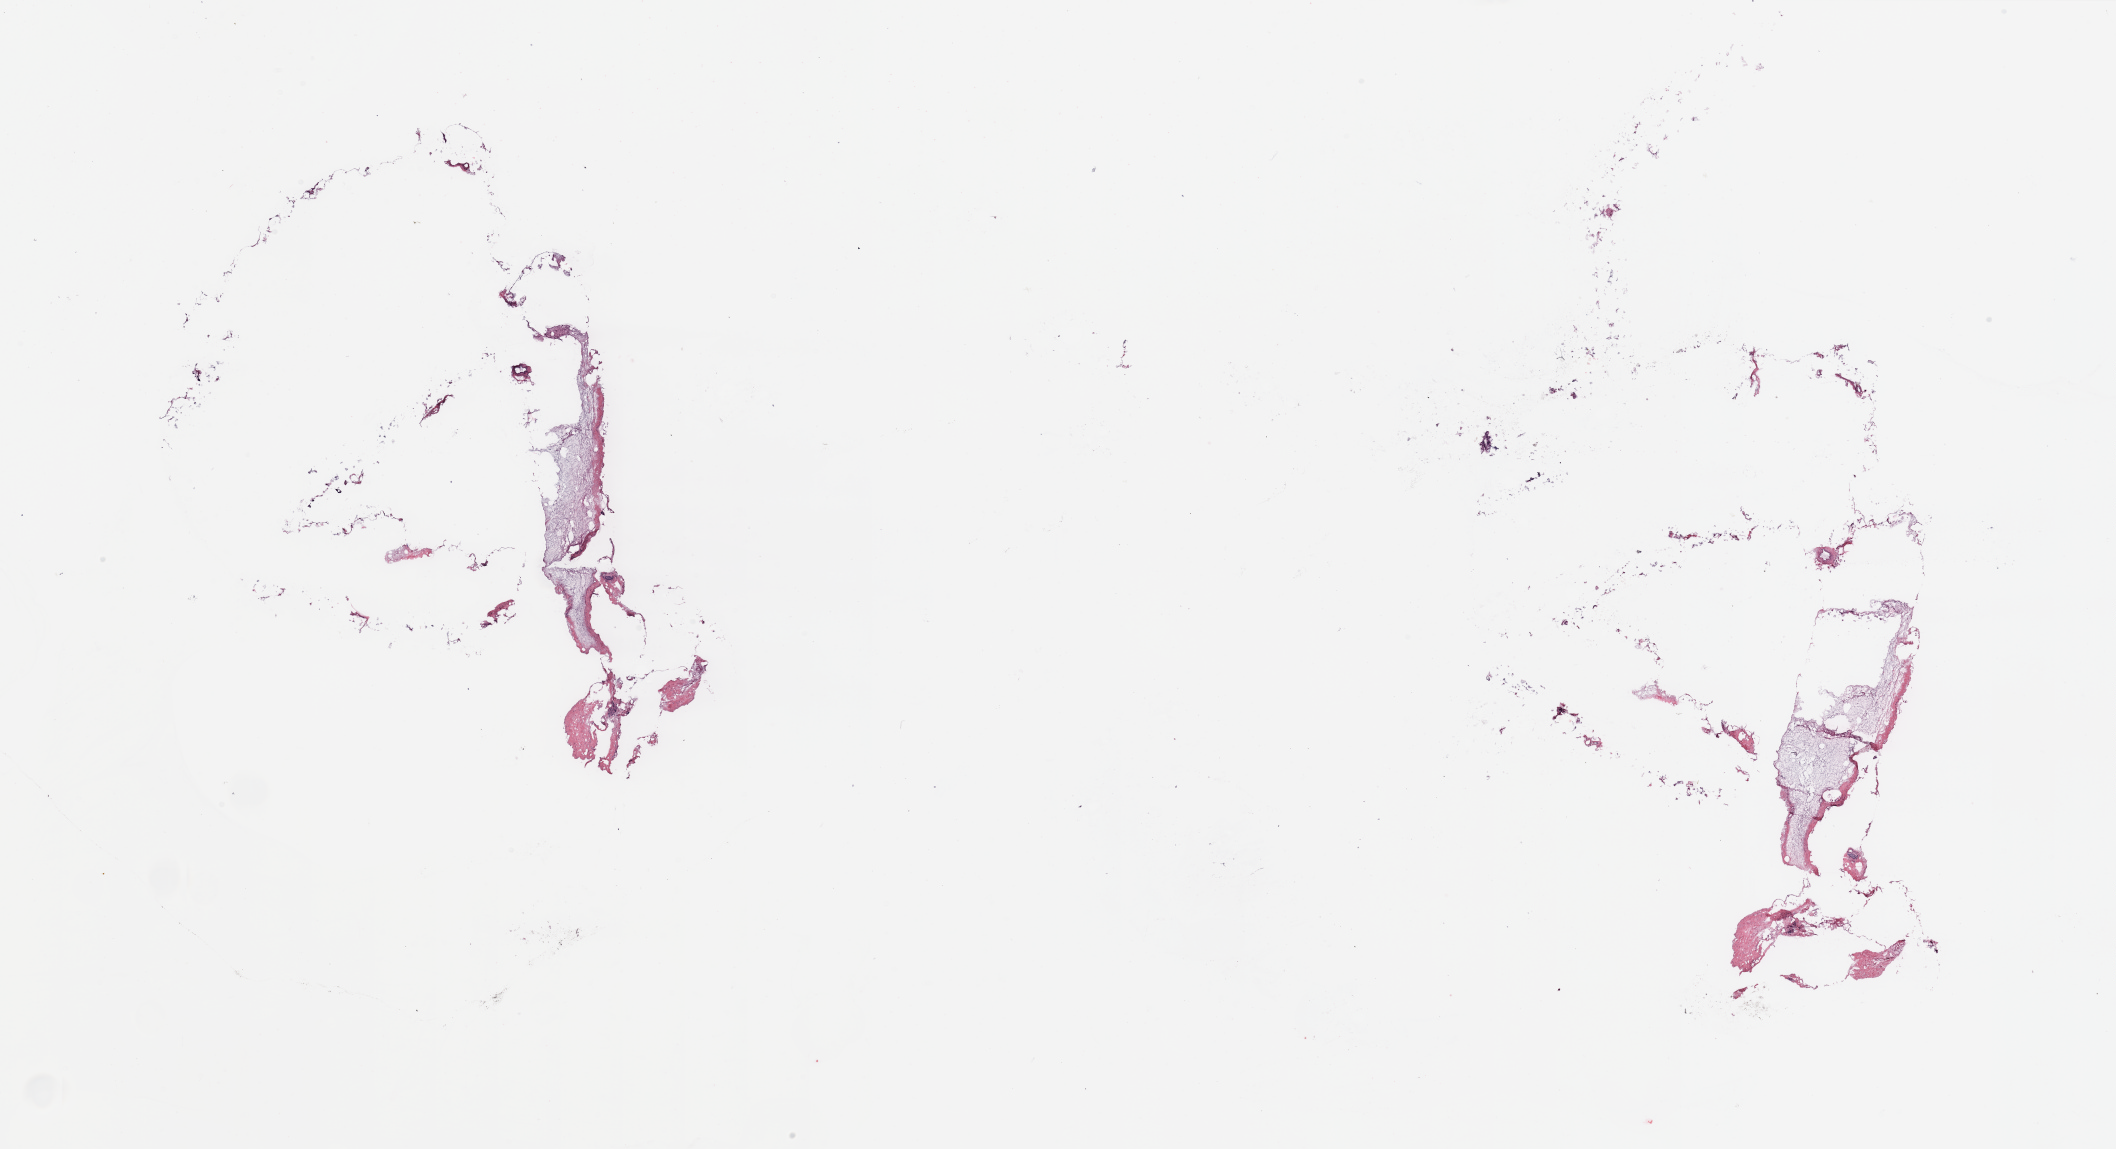
Digitized Hematoxylin and eosin (H&E) stained tissue section (whole slide), a low-resolution overview of the entire scanned area, about 33.5 x 18.2 mm (from a 20x scan); tumour tissue sample, breast. 80-year-old female patient.
• AJCC pathologic stage: IIA
• histologic diagnosis: Infiltrating duct carcinoma, NOS